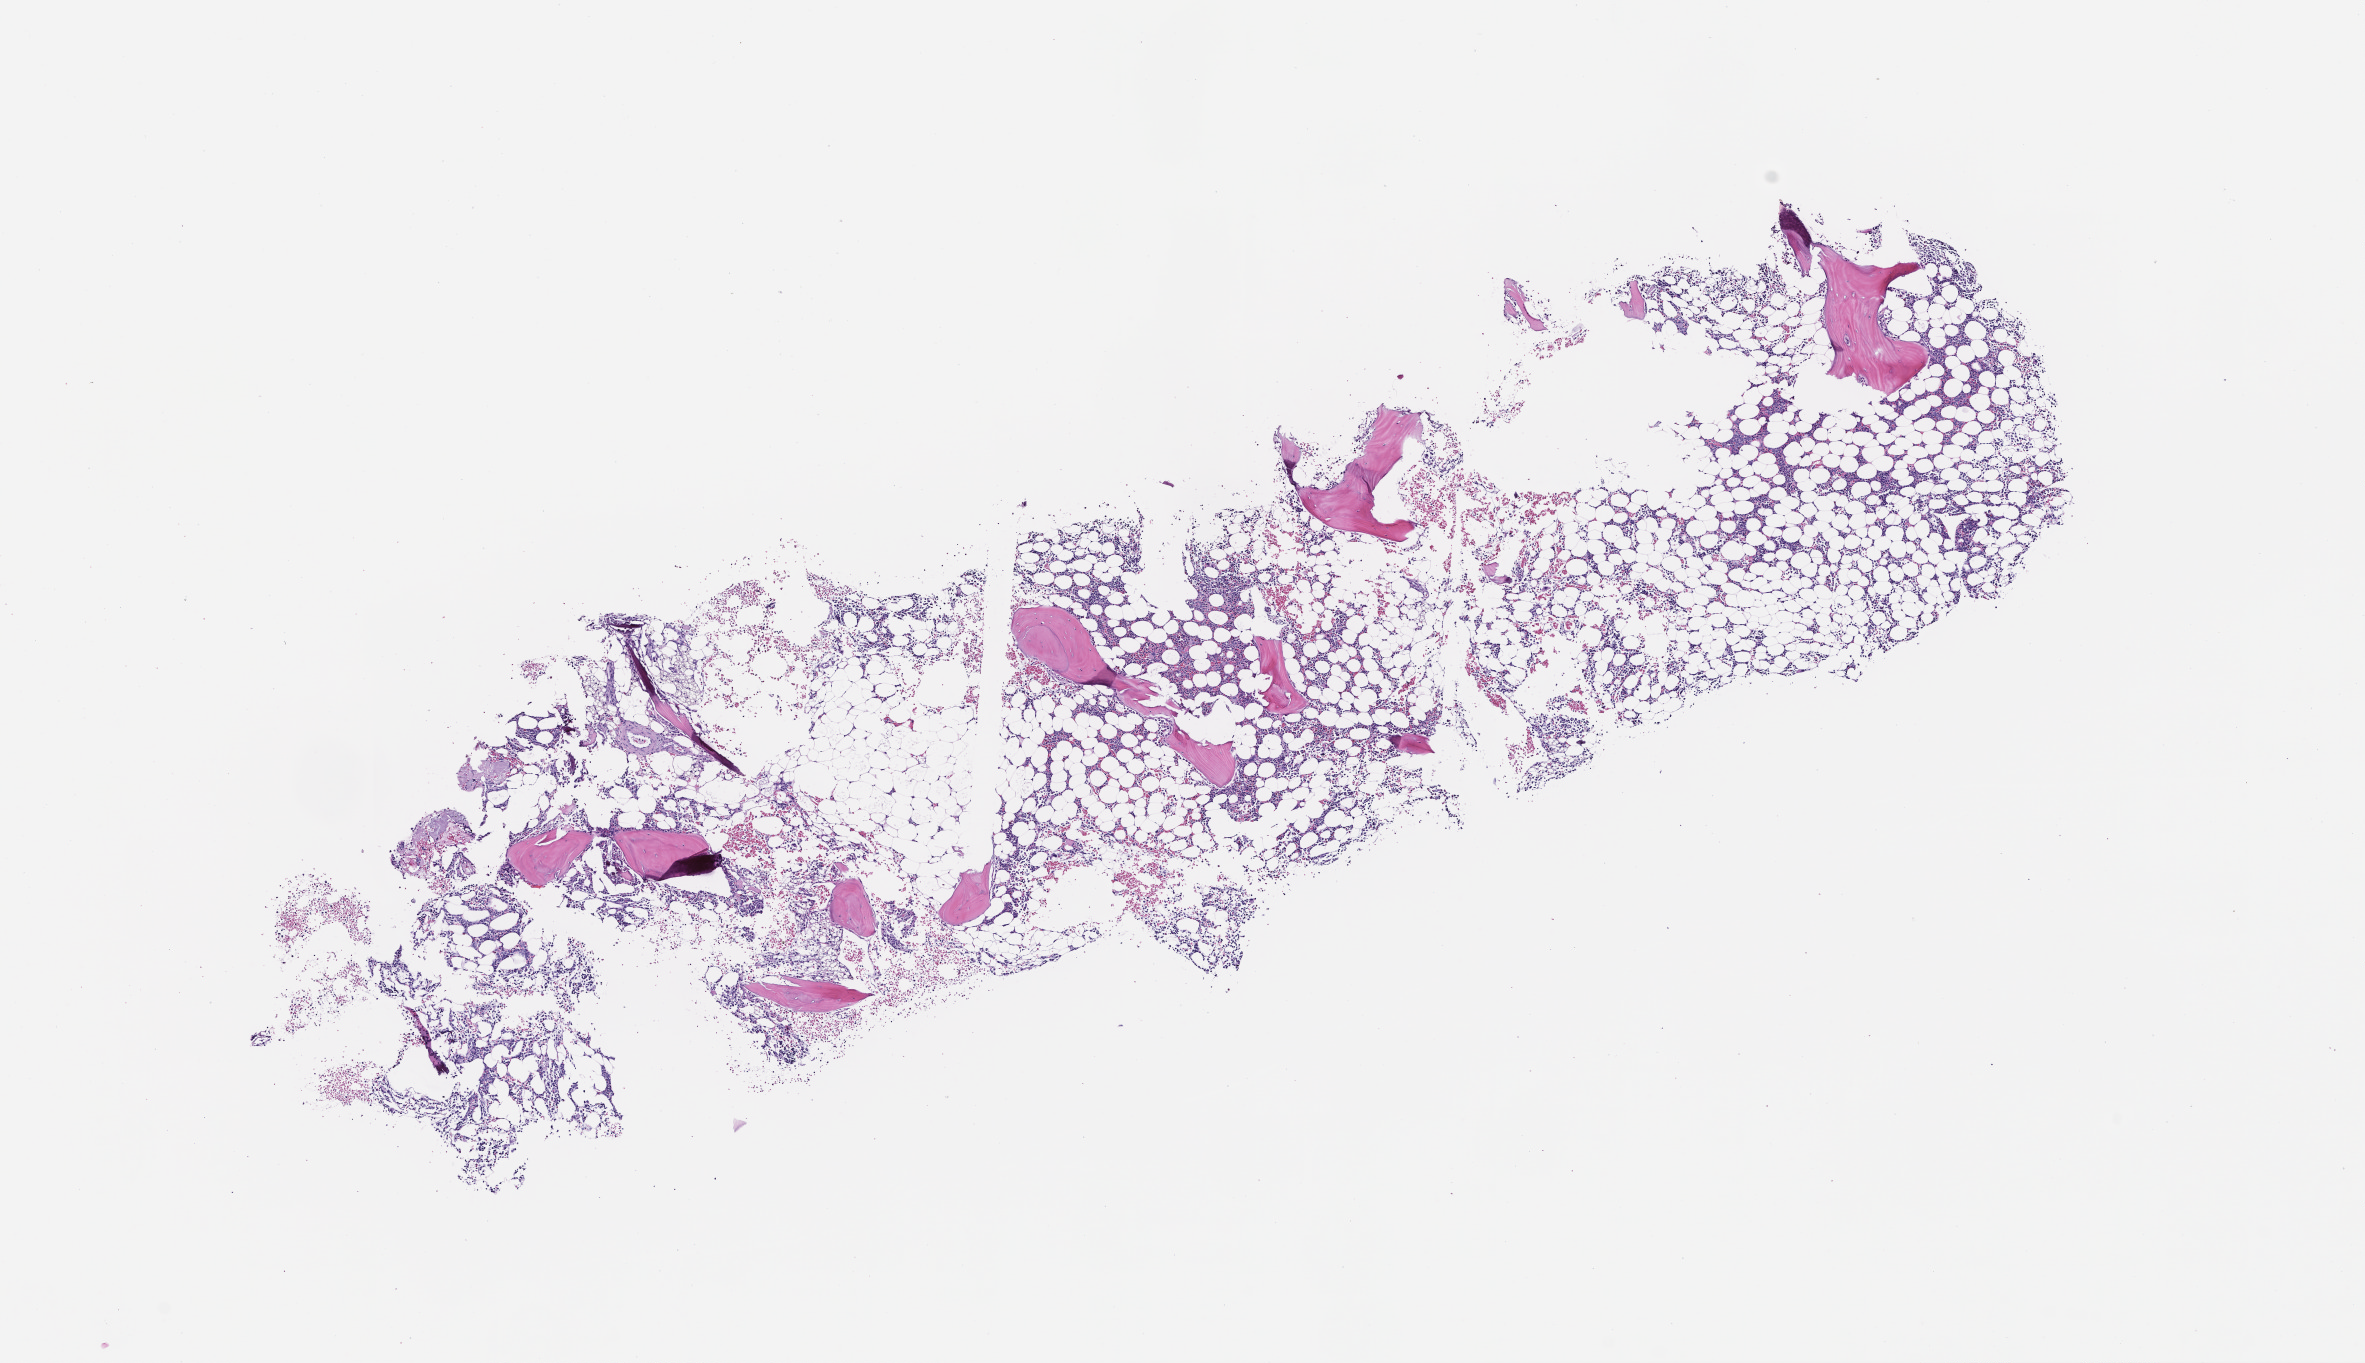
H&E whole-slide image, whole scanned area (about 9.5 x 5.5 mm) shown as a low-resolution overview. FFPE section. Tissue site: bone marrow. Specimen time point: collected at baseline (before treatment). Patient: male.
• this section: primary tumour tissue
• diagnosis: Plasma Cell Myeloma